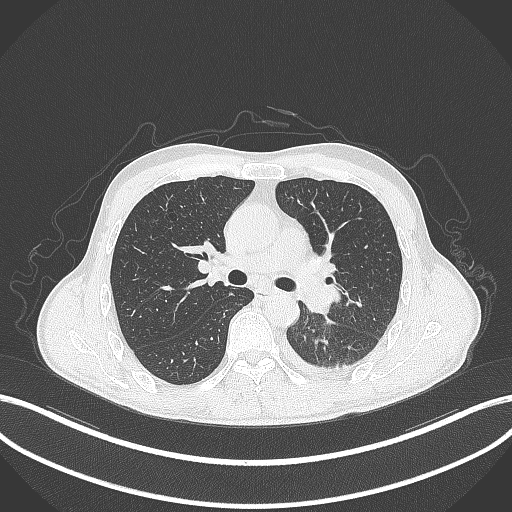
Chest CT, one axial slice; position 200 of 295 along the scan axis; lung window (W 1500 / L -600 HU); 1 mm slice thickness; 512 × 512 image matrix. Male patient, age 47 years. Case-level facts recorded for this patient, not image findings: clinical TNM (as recorded): T3 N1 M1c.
Structures marked on this image (rectangle marked by the reading radiologist):
- lung tumour (recorded histology: small cell carcinoma): bounding box [x1, y1, x2, y2] px = [294, 278, 343, 316]